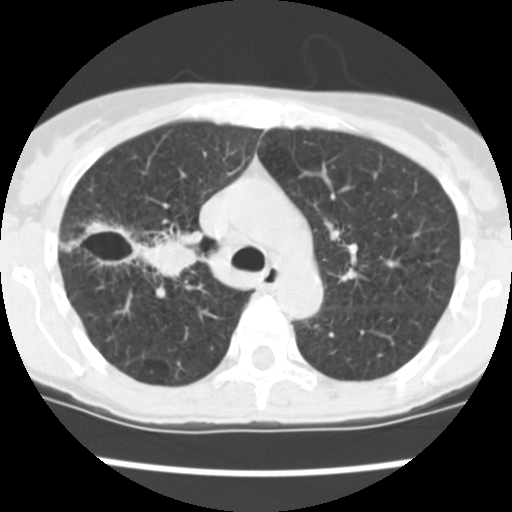
Low-dose screening chest CT, one axial slice; reconstruction kernel STANDARD; lung window (W 1500 / L -600 HU); 2.5 mm slice thickness; 512 × 512 image matrix, field of view 276 × 276 mm.
Annotated regions visible in this slice (expert manual segmentation):
- lesion 2 (tumor, lower lobe of right lung): bounding box <80,221,203,278> (left, top, right, bottom; pixels)